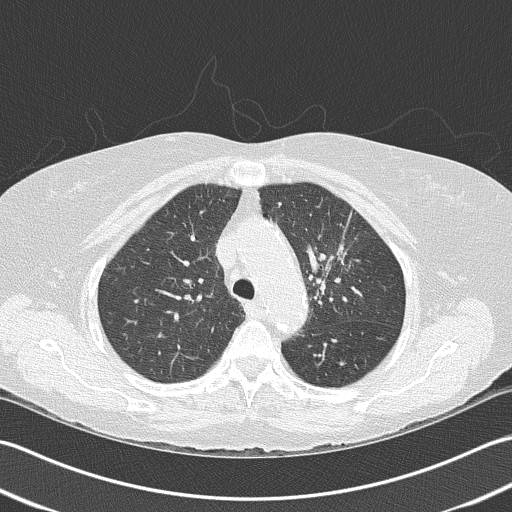
Axial slice from a low-dose chest CT screening exam. Baseline annual screen. Lung window (W 1500 / L -600 HU). 2 mm slice thickness. 120 kVp. Female participant, aged 68 years at enrolment. Former smoker at enrolment.
Lesion marked by an expert reader, bounding box (x1, y1, x2, y2) in pixels: (297, 212, 373, 301). Screening reader's record for this exam: no non-calcified nodule ≥4 mm recorded. Official screen result: negative screen, minor abnormalities not suspicious for lung cancer. Lung cancer was diagnosed 763 days after this screen: adenocarcinoma, NOS, left upper lobe, poorly differentiated (G3), stage IB (AJCC 6th edition), 50 mm at pathology.